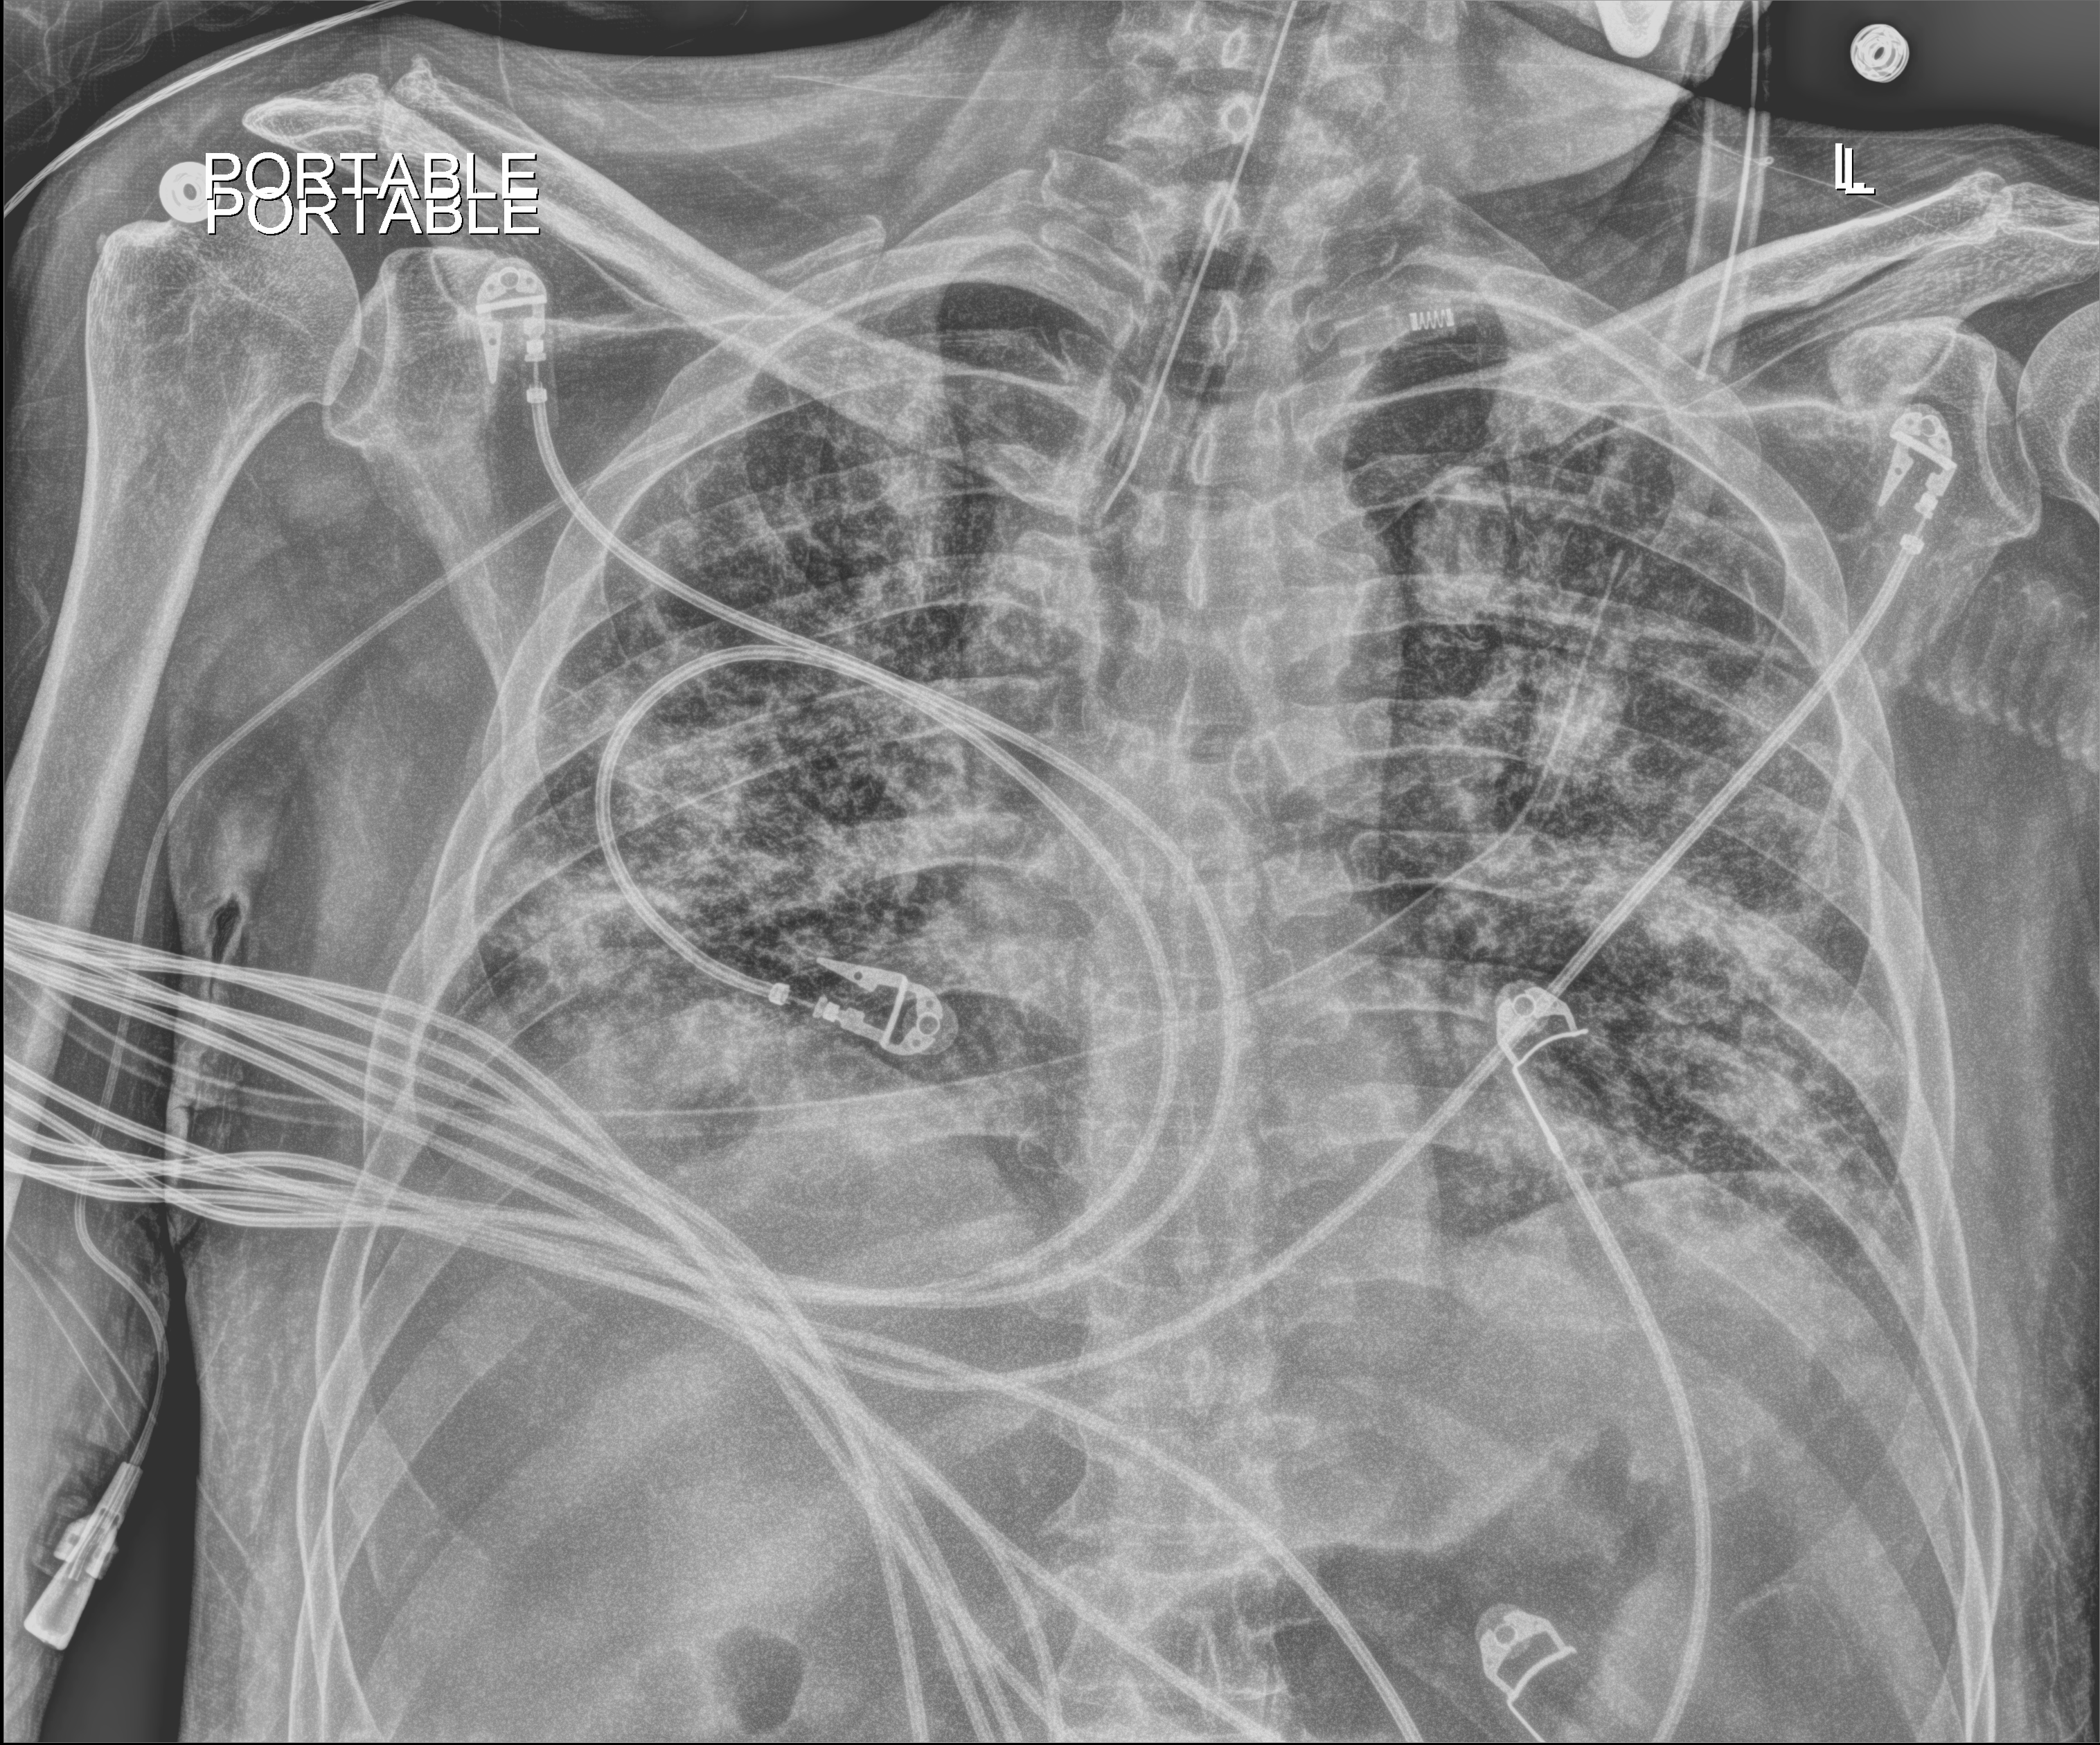
Bedside chest radiograph (digital radiography); anteroposterior (AP) projection. Male patient hospitalised with COVID-19, age 18–59 years.
Hospital-stay facts (about this admission, not read from this image; timing relative to this image not recorded): admitted to intensive care during this hospital stay: yes; other chronic lung disease (admission record): no; mechanically ventilated during this hospital stay: yes.